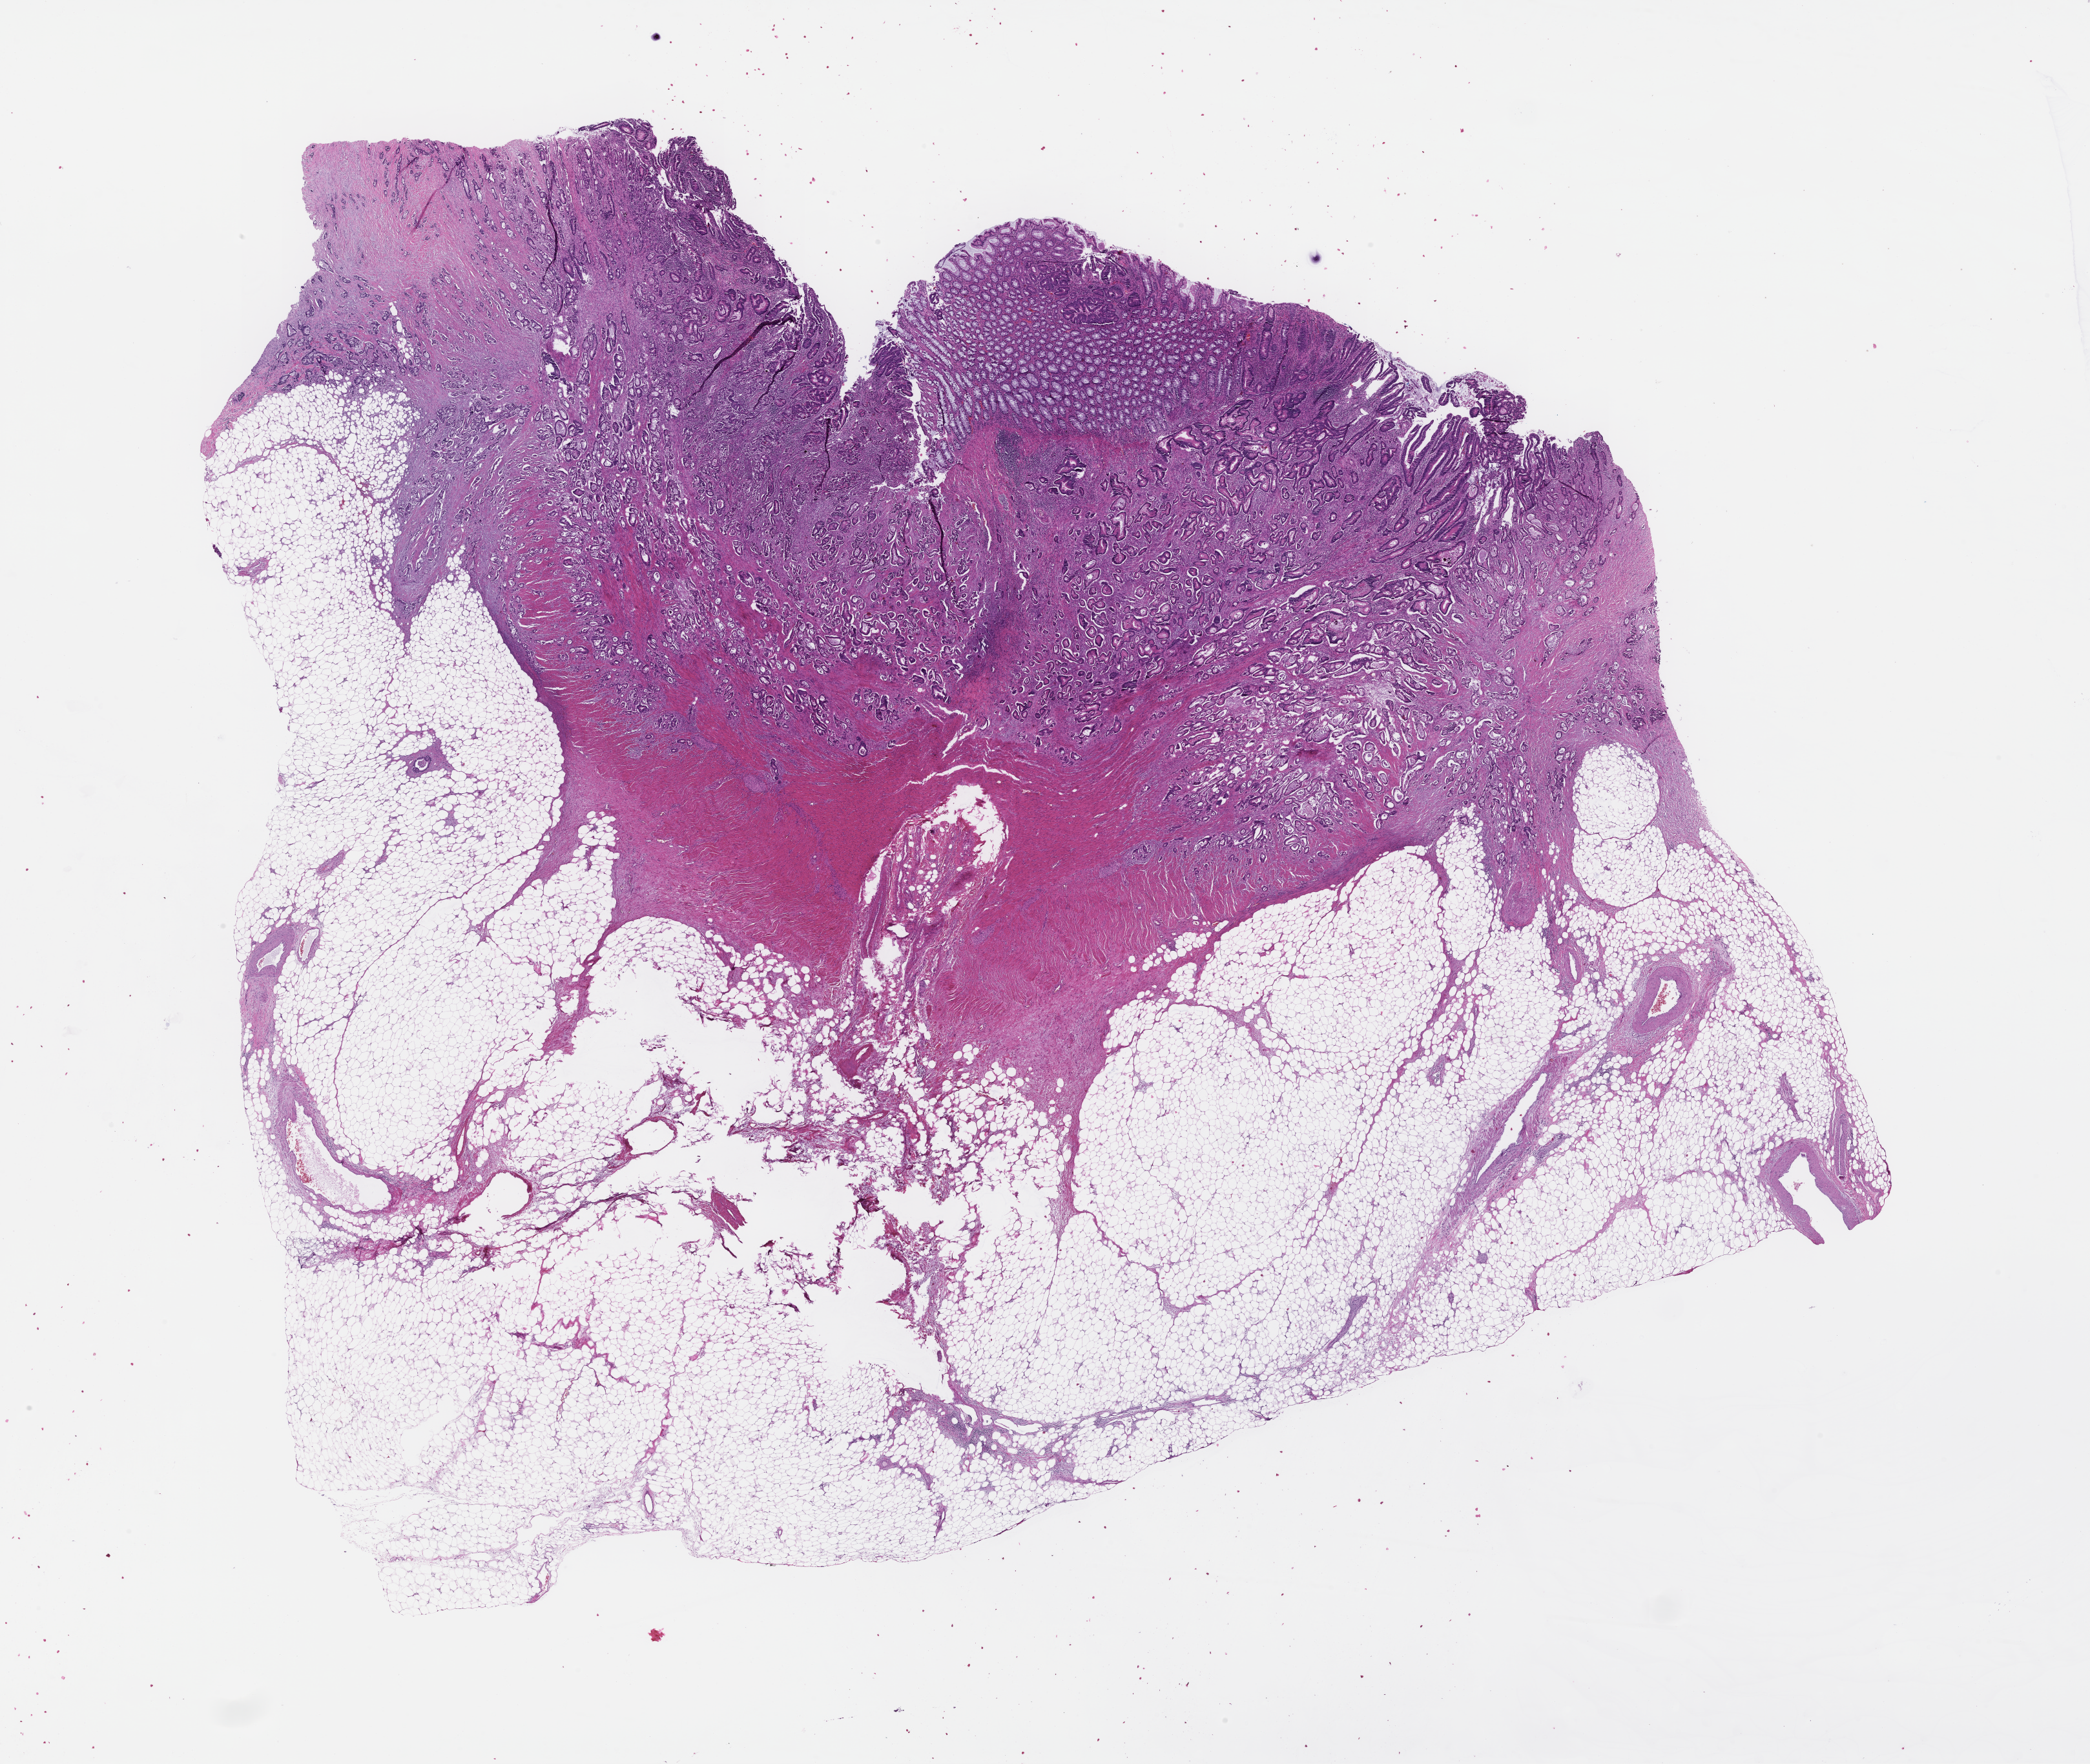
Haematoxylin and eosin whole-slide image, whole scanned area (about 26.1 x 22.1 mm) shown as a low-resolution overview, formalin-fixed, paraffin-embedded (FFPE) tissue, tissue site: colon, specimen time point: archival tissue. Patient: female.
This section: primary tumour tissue. Diagnosis: Colorectal Carcinoma.